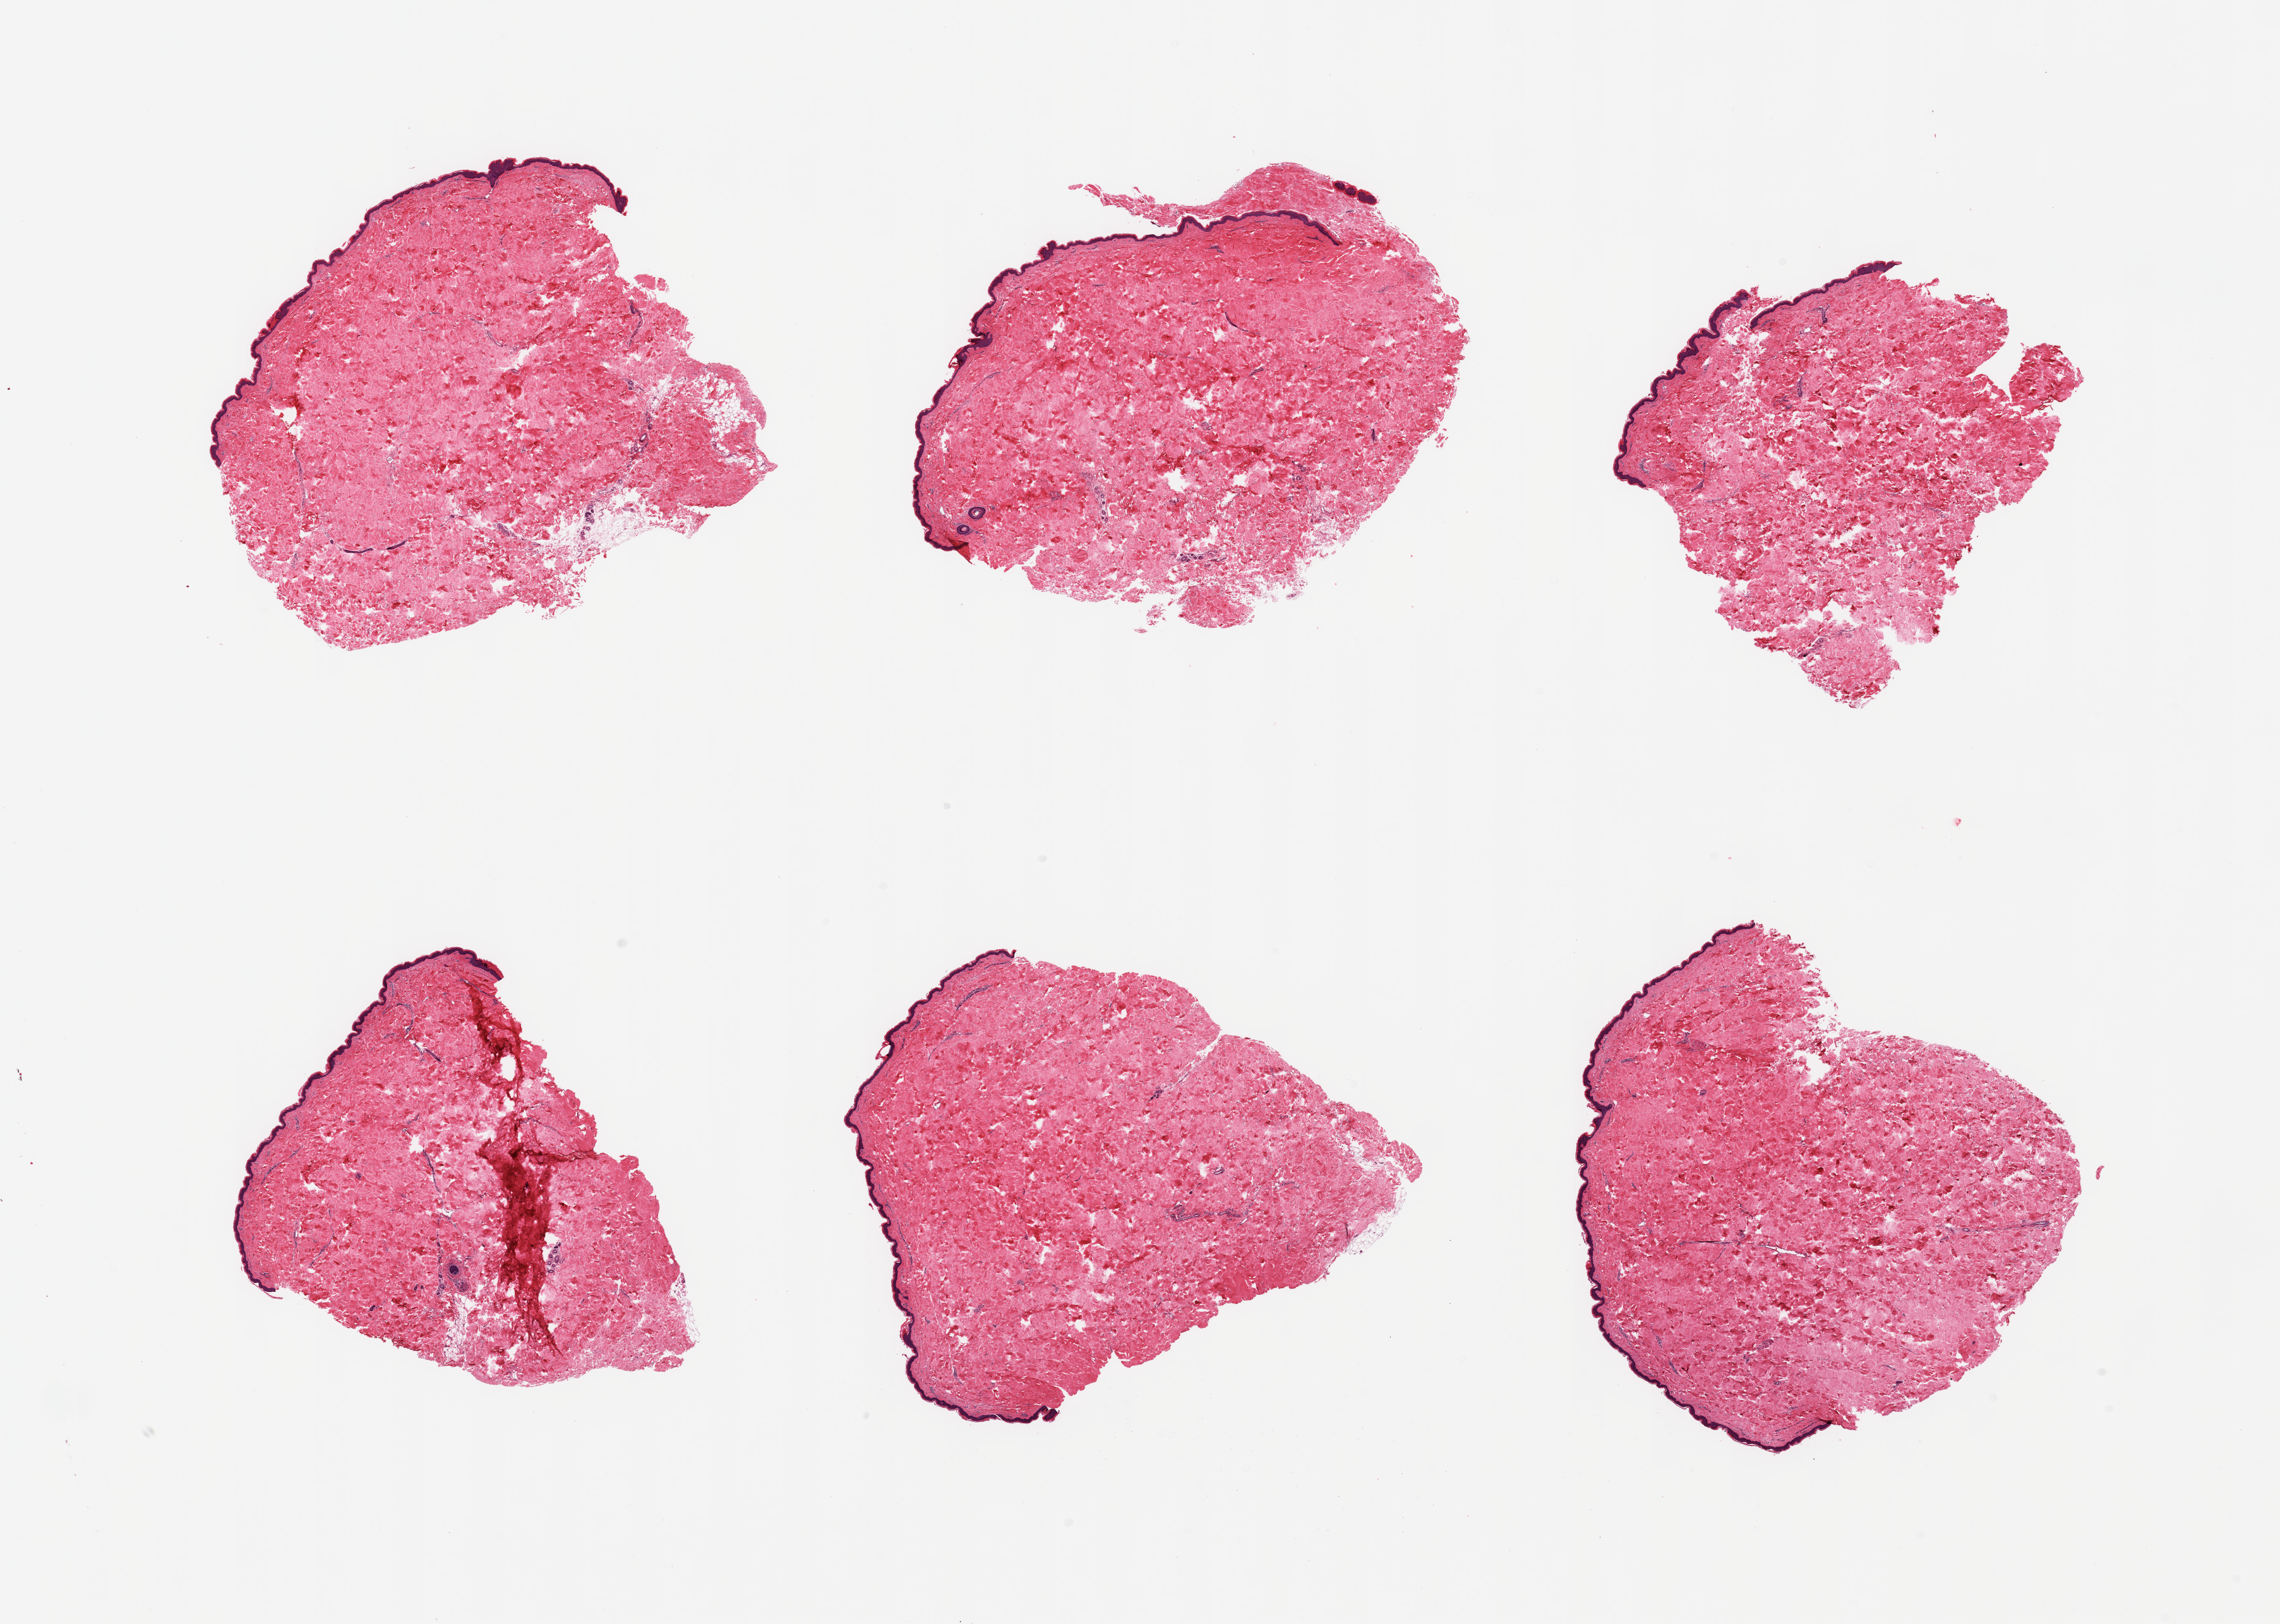
Digitized haematoxylin and eosin-stained section, whole scanned area (about 28.5 x 20.3 mm) shown as a low-resolution overview. PAXgene-fixed, paraffin-embedded tissue. Section of skin of suprapubic region (target tissue). Tissue donor sample. Donor sex: female.
- review note (as recorded): 6 pieces, no dermal fat; squamous epithelium is ~35-45 microns